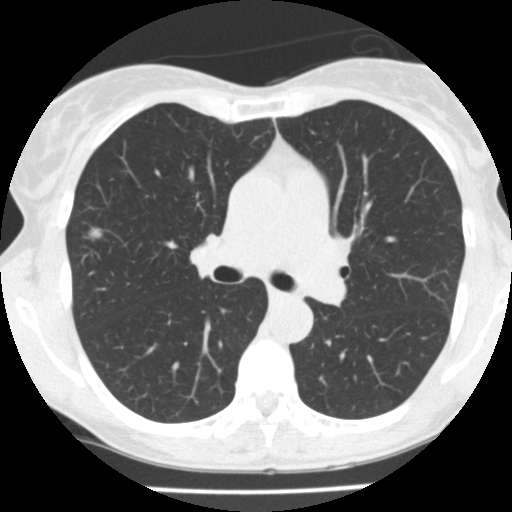
Low-dose screening chest CT, one axial slice; position 104 of 166 along the scan axis; reconstruction kernel FC10; lung window (W 1500 / L -600 HU); 2 mm slice thickness; 512 × 512 image matrix, field of view 280 × 280 mm.
Annotated regions visible in this slice (manually delineated by an expert):
- lesion 1 (tumor, upper lobe of right lung): box from (x=90, y=228) to (x=102, y=238) px